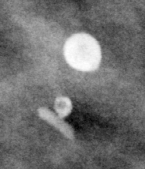
Crop from a digitized film mammogram around one marked abnormality; left breast; MLO view.
- Calcifications, morphology large rodlike / round and regular, distribution regional; BI-RADS assessment category 2; benign without callback (not worked up further).